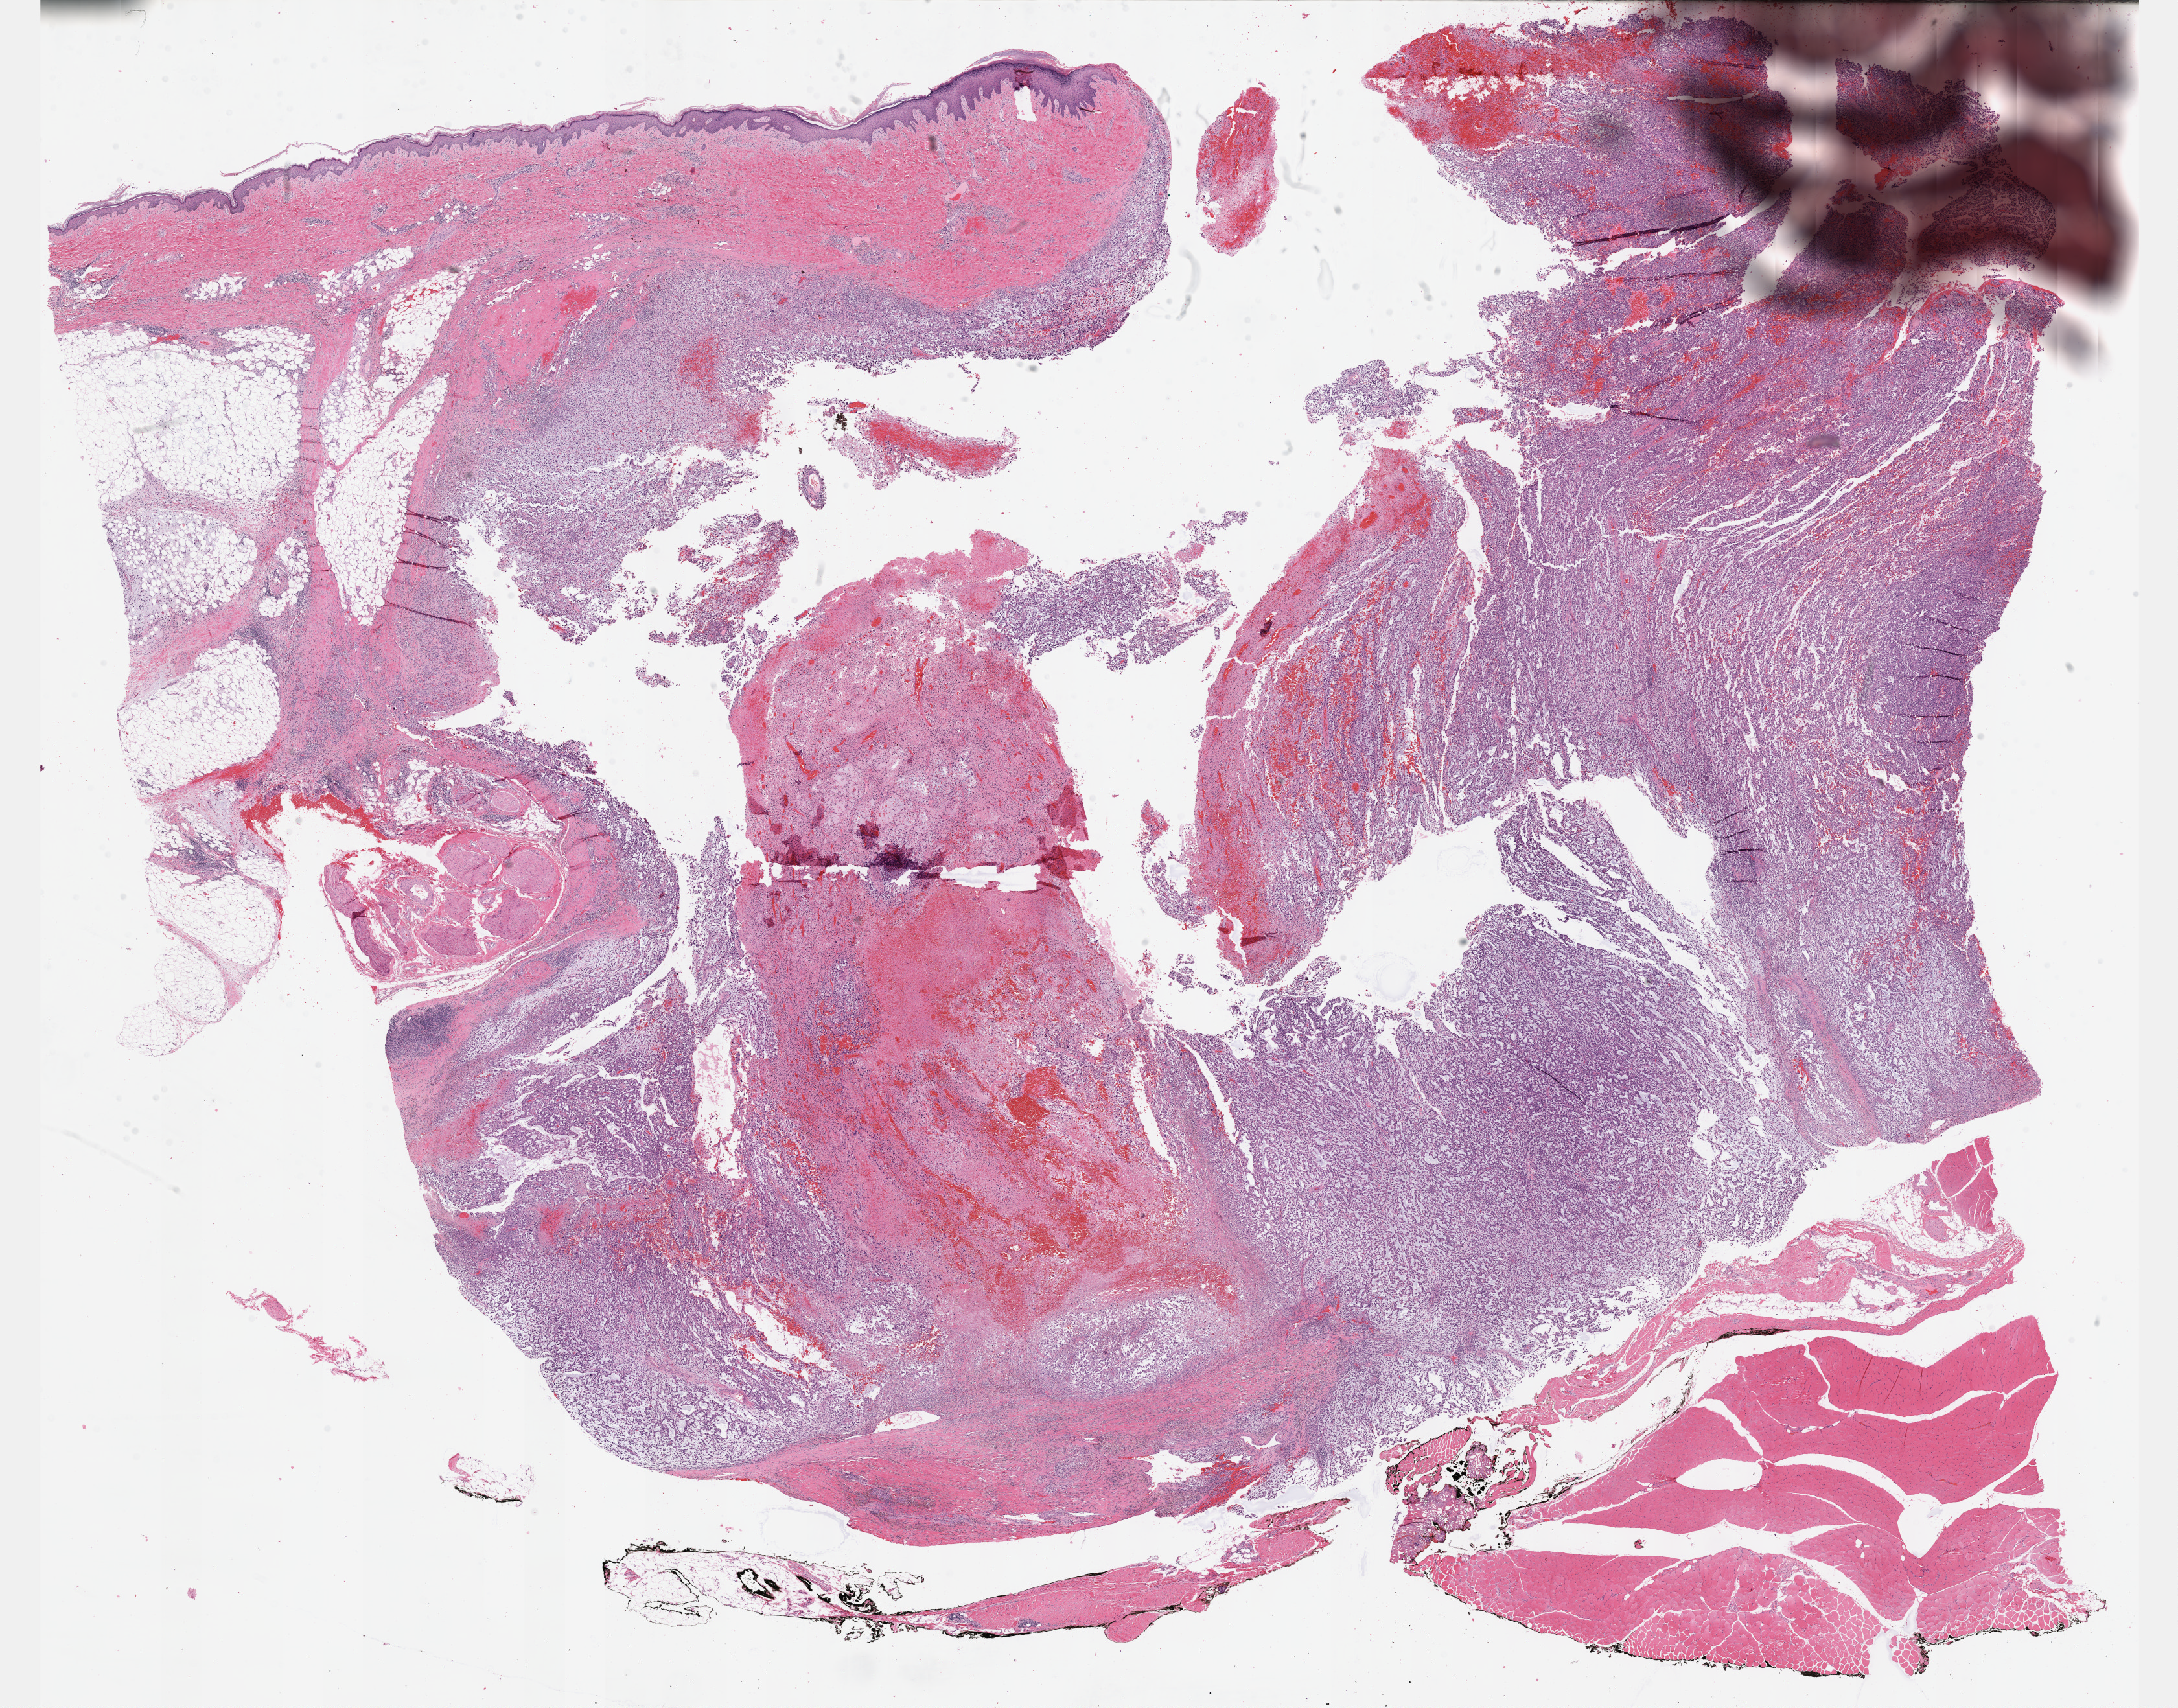
Digitized H&E-stained tissue section (whole slide), shown as a low-resolution overview of the whole scanned area (about 27.2 x 21.3 mm, slide scanned at 40x); formalin-fixed paraffin-embedded (FFPE) diagnostic section; sample: primary tumour, connective, subcutaneous and other soft tissues. Female patient; age at initial diagnosis 59 years.
• diagnosis: Fibromyxosarcoma (connective, subcutaneous and other soft tissues of lower limb and hip)